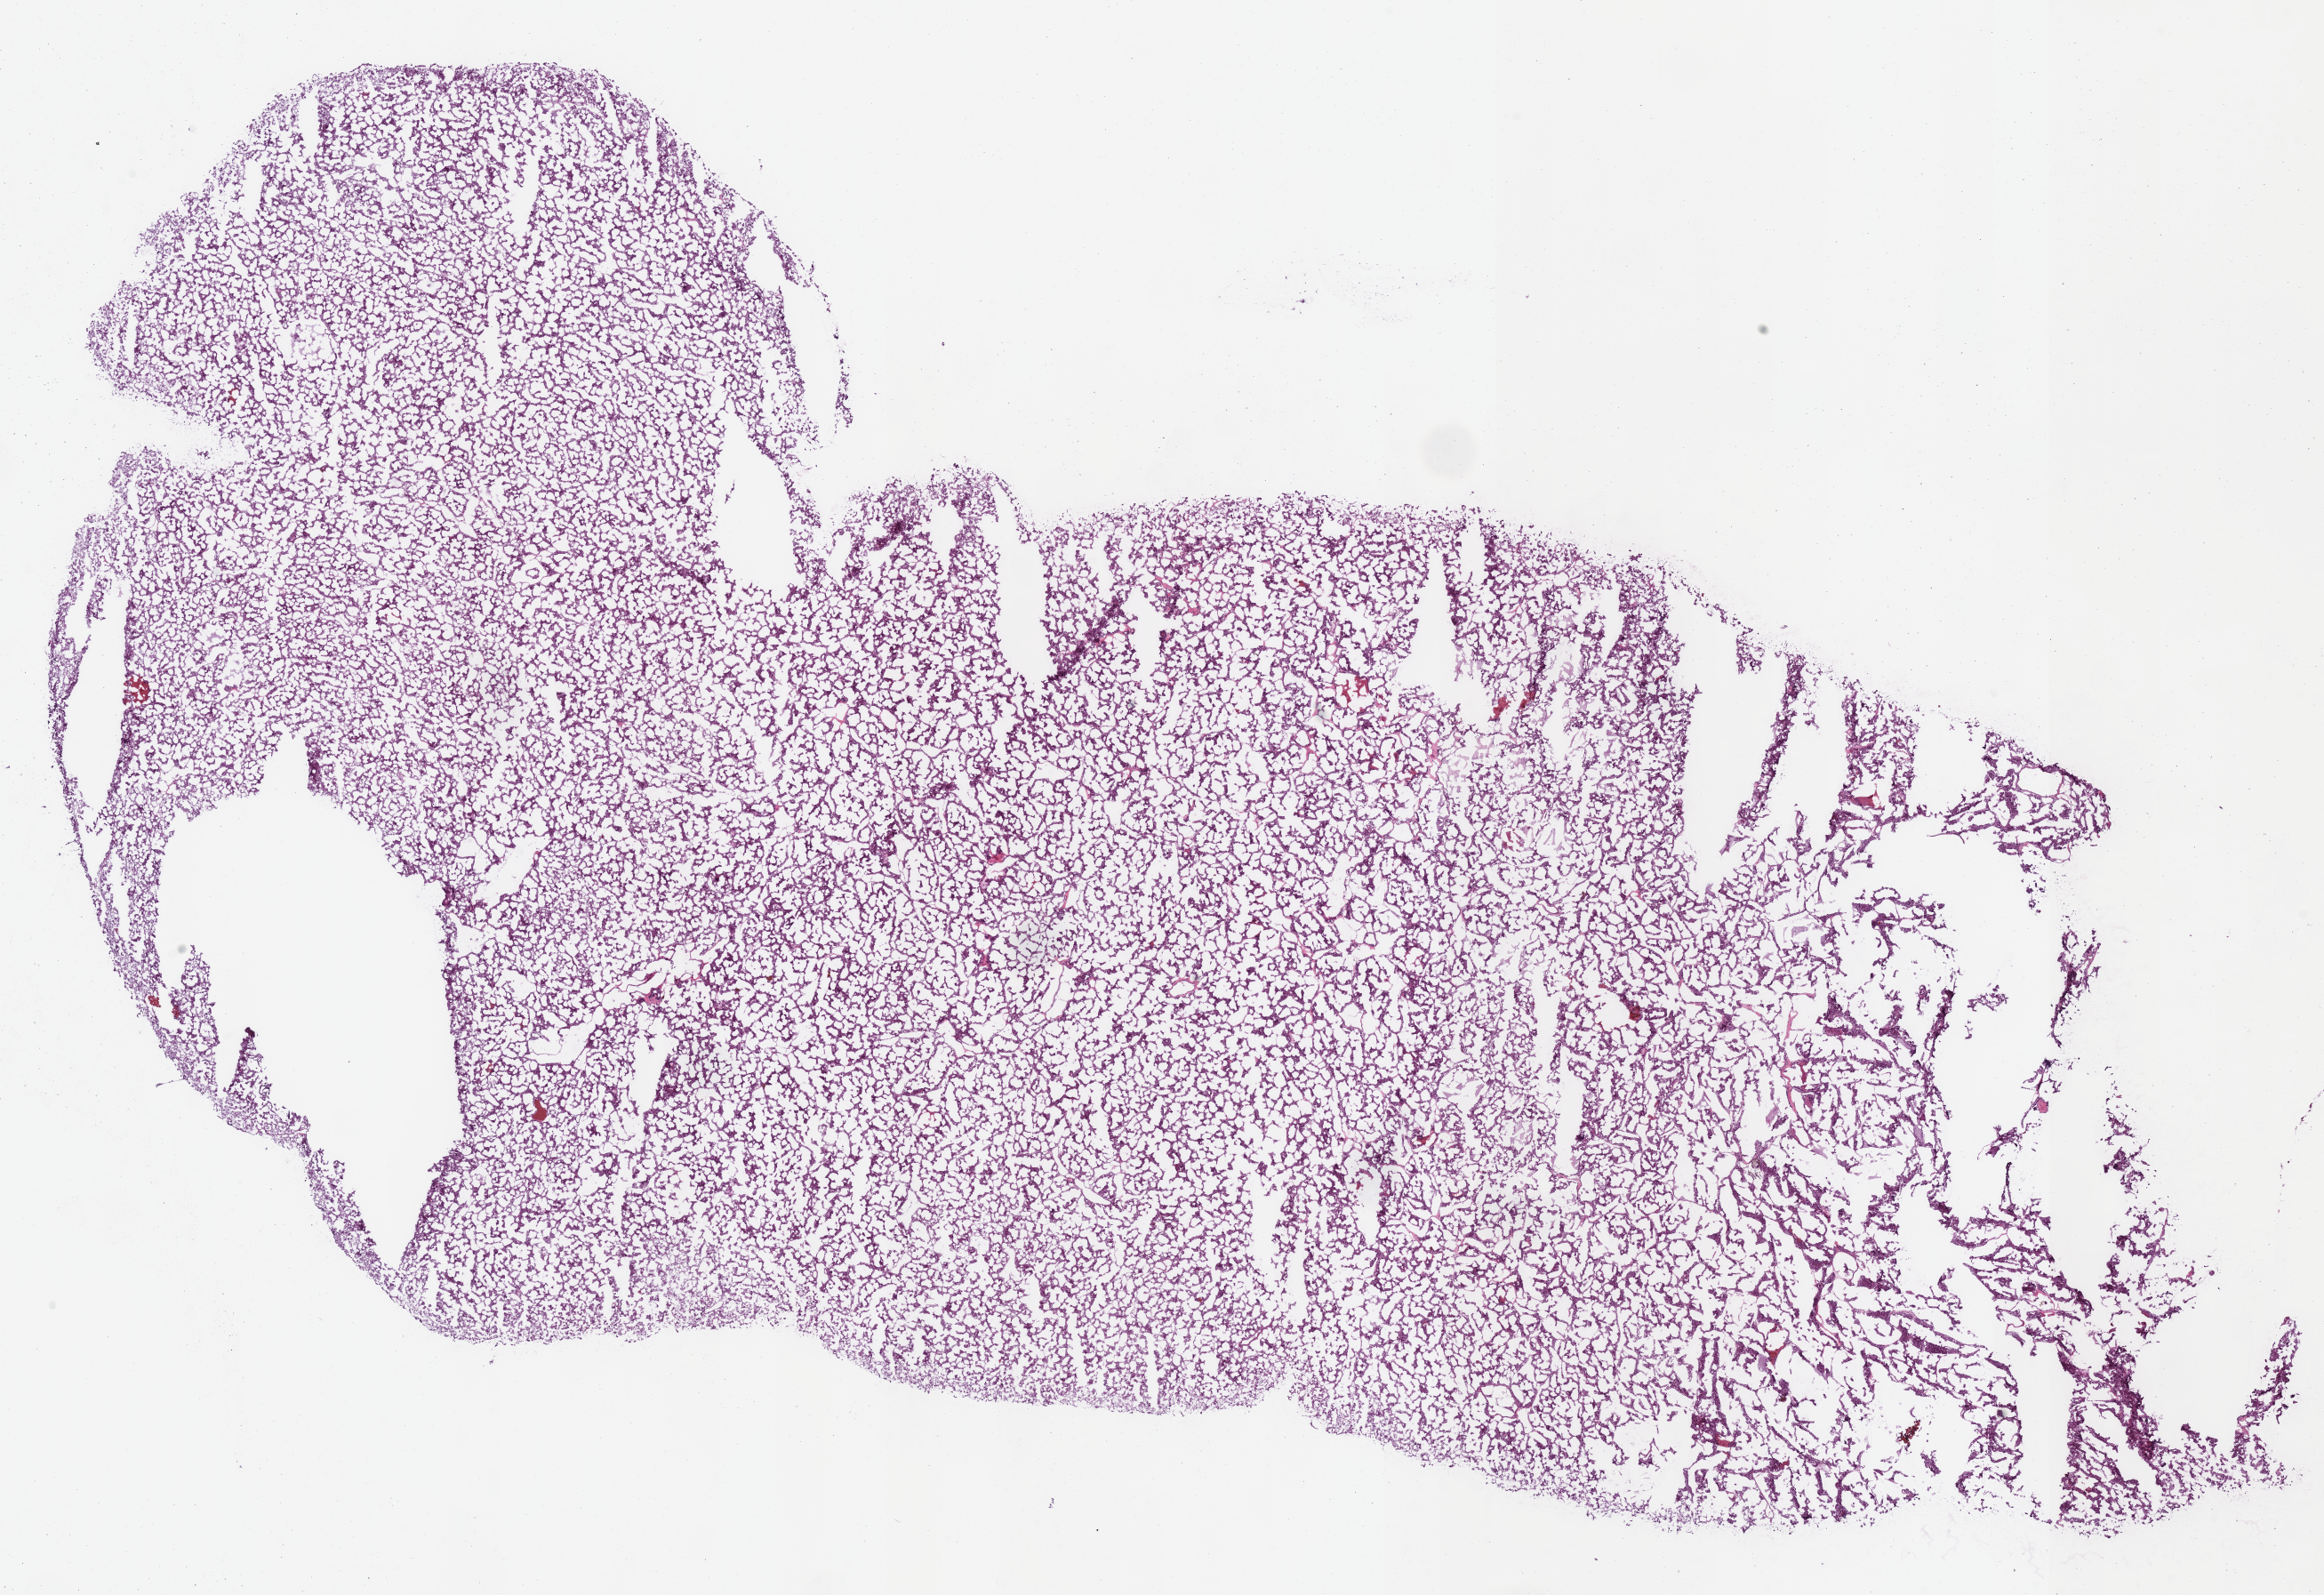
Hematoxylin and eosin (H&E) stained whole-slide image — a low-resolution overview of the entire scanned area, about 20.6 x 14.1 mm. Frozen section. Kidney, primary tumour sample. Patient: female, age at initial diagnosis 46 years. Composition of this section per pathologist review: tumour cells 100%, tumour nuclei 90%, normal cells 0%, stromal cells 0%, necrosis 0%. Infiltration values recorded for this section: lymphocyte infiltration 1%, monocyte infiltration 0%, neutrophil infiltration 0%.
- histologic diagnosis: Renal cell carcinoma, chromophobe type
- AJCC pathologic stage: I
- lymph nodes positive (case pathology): 0 of 3 examined